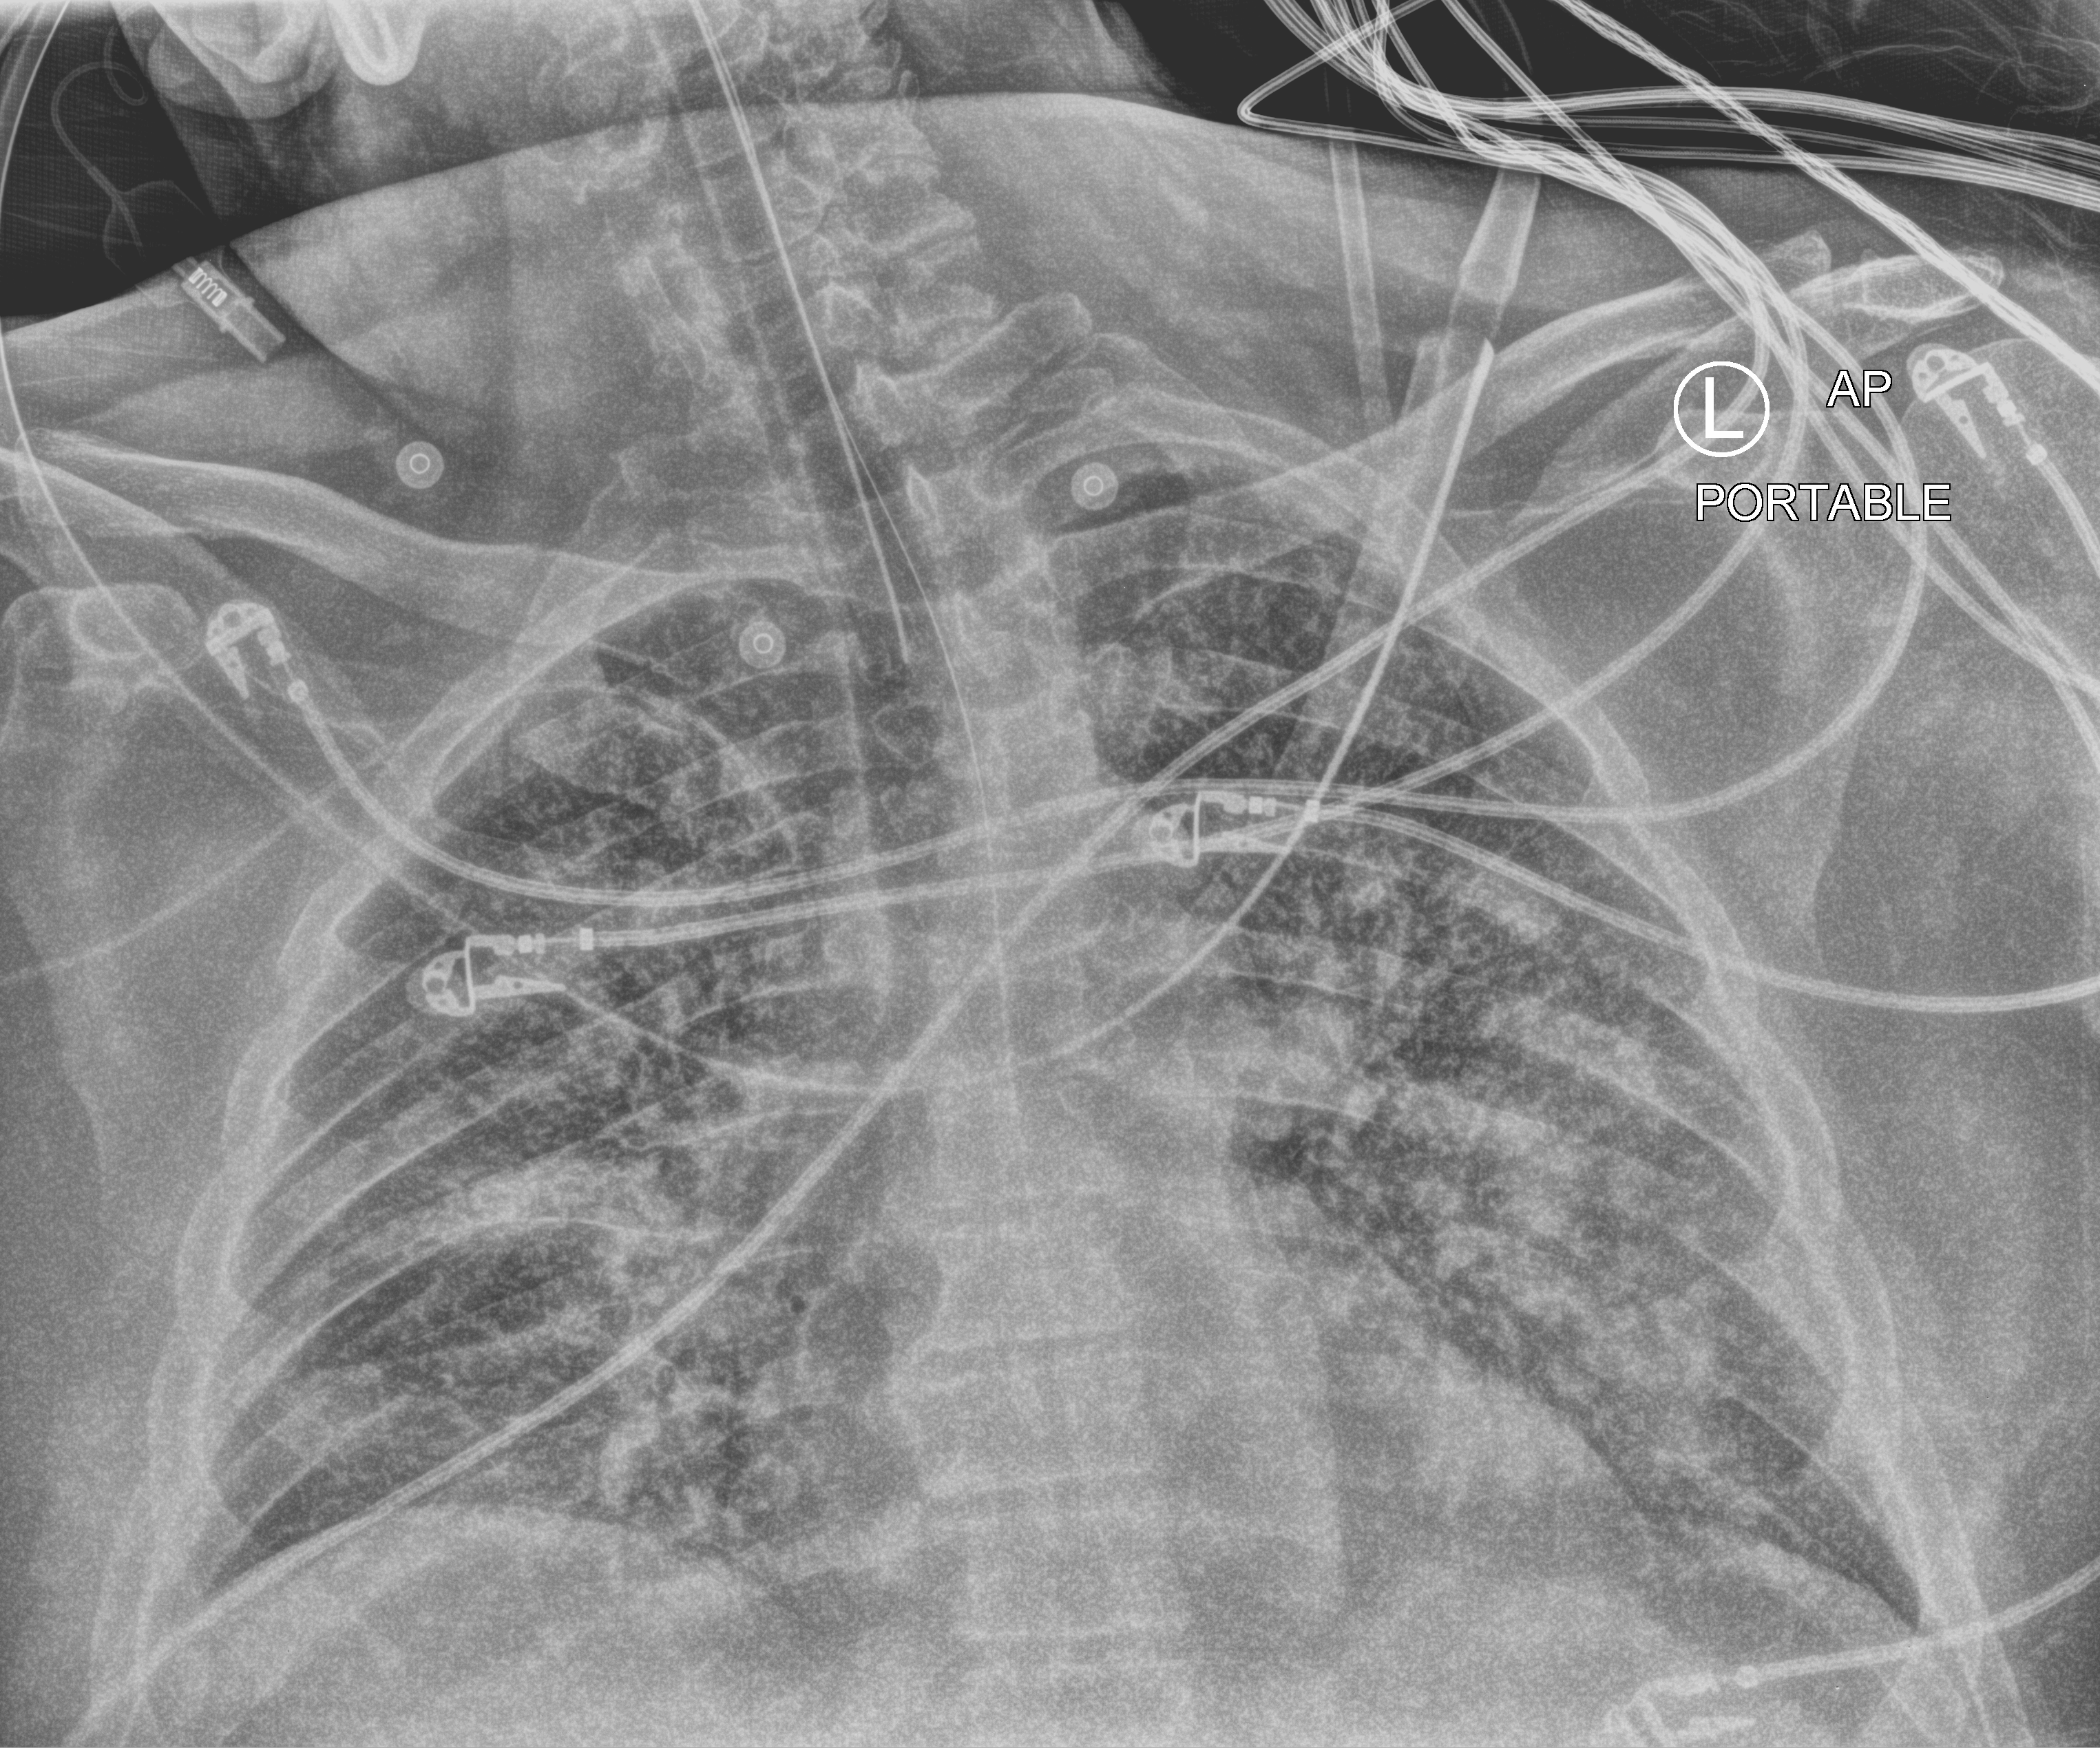
Chest X-ray (portable); anteroposterior (AP) projection. Patient hospitalised with COVID-19; male, aged 60–74 years.
Hospital-stay facts (about this admission, not read from this image; timing relative to this image not recorded):
- length of hospital stay: 13 days
- chronic kidney disease (admission record): no